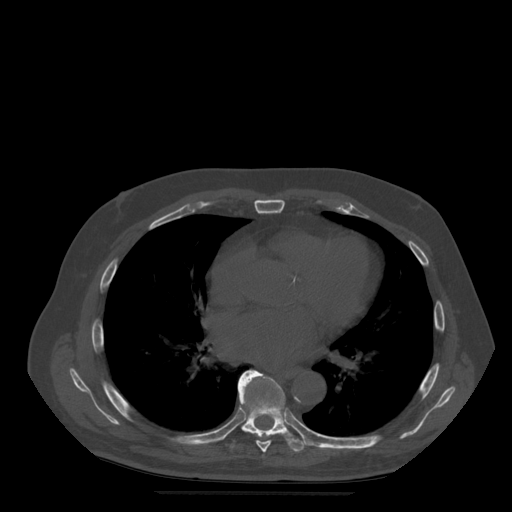
CT including the spine, one axial slice. Position 322 of 522 along the scan axis. Bone window (W 1800 / L 400 HU). 1.25 mm slice thickness. 512 × 512 image matrix, field of view 420 × 420 mm. Patient age 72 years. Case-level facts recorded for this patient, not image findings: primary cancer: prostate.
Structures marked on this image (semi-automatically segmented with operator editing):
- T7 vertebra: bounding box <238,372,272,453> (left, top, right, bottom; pixels)
- T8 vertebra: <228,370,309,452>